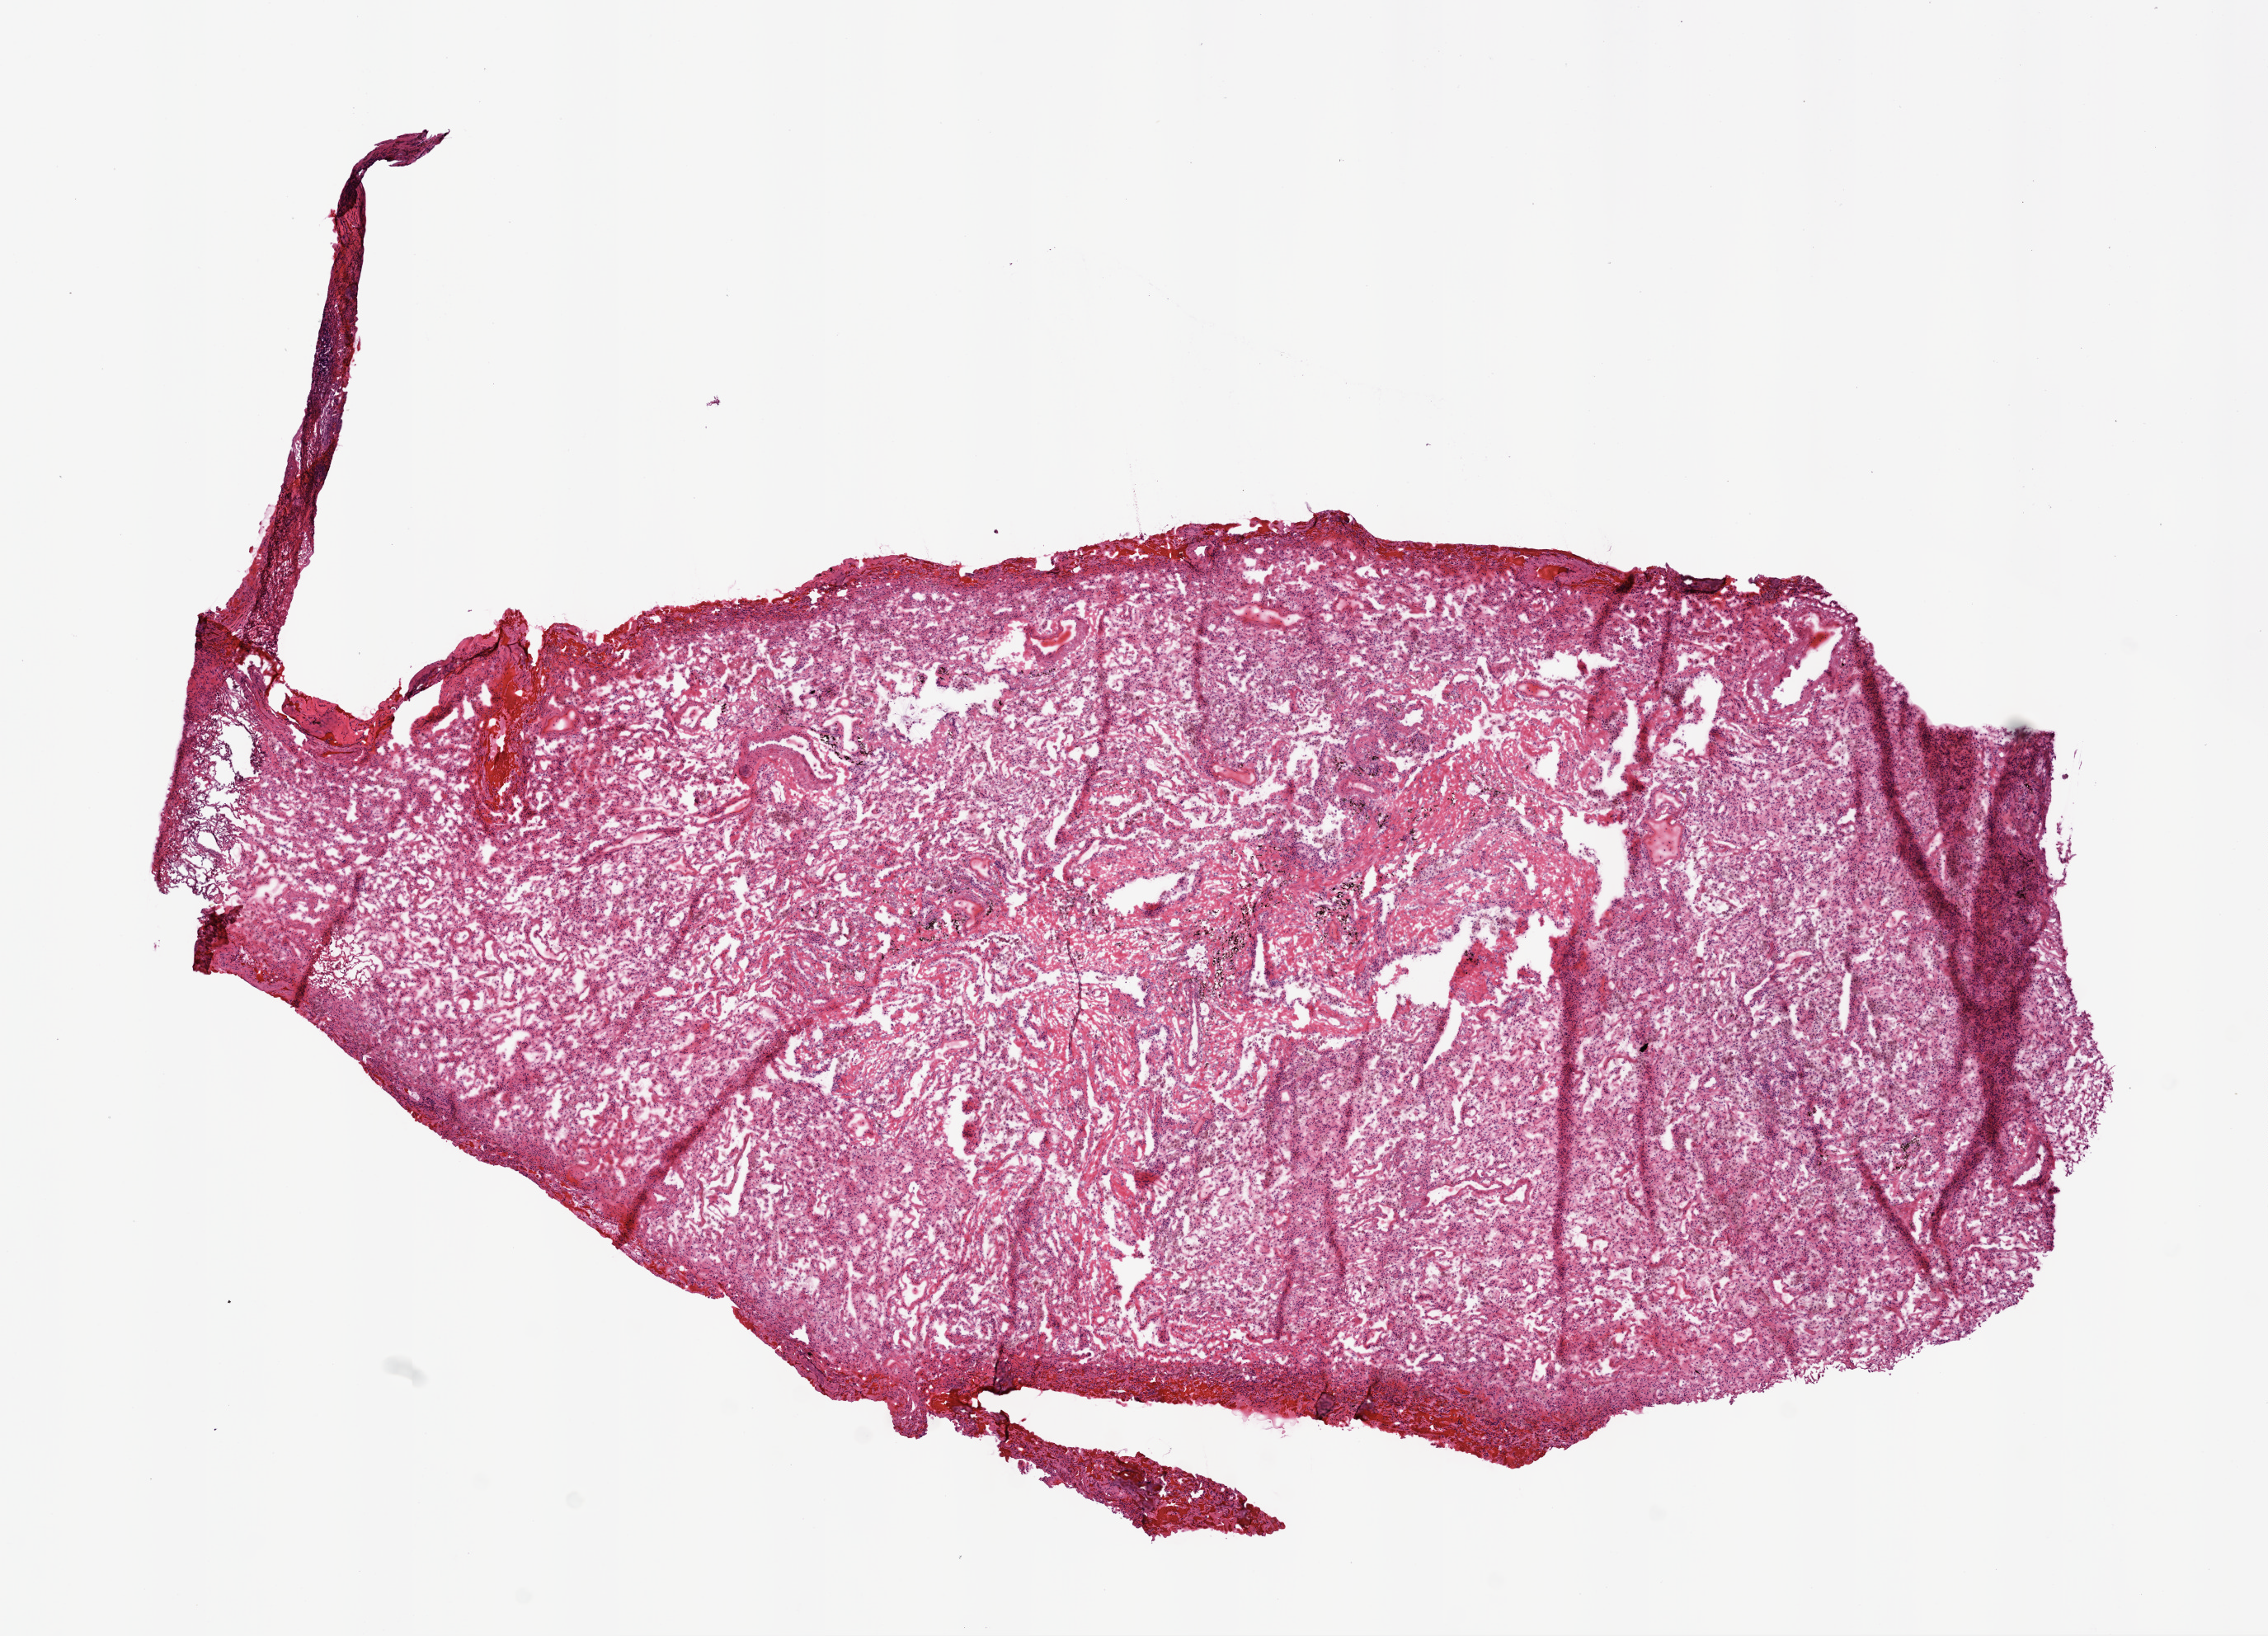
H&E-stained whole-slide image — shown as a low-resolution overview of the whole scanned area (about 11.0 x 8.0 mm, from a 20x scan), frozen section from the bottom of the tissue portion, solid tissue normal (non-tumour tissue) sample from the lung. Patient: male, age at initial diagnosis 45 years.
* this section: solid tissue normal (non-tumour) sample from the same patient
* patient diagnosis: Adenocarcinoma, NOS